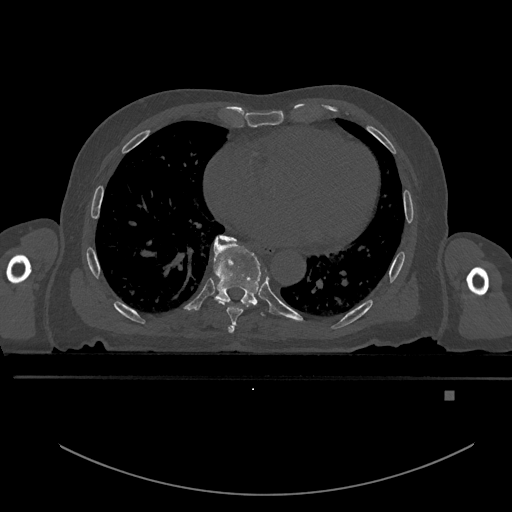
CT including the spine, one axial slice. Slice 226 of 969 in the series (ordered by position). Bone window (W 1800 / L 400 HU). 0.5 mm slice thickness. 512 × 512 image matrix, field of view 456 × 456 mm. Male patient, age 82 years. From the clinical record (not read from this slice): primary cancer: prostate; vertebrae with lytic lesions (as recorded): T11, T9, T8, T2.
Annotated regions visible in this slice (semi-automatically segmented with operator editing):
- T6 vertebra: box from (x=228, y=326) to (x=234, y=333) px
- T7 vertebra: (x=218, y=235)–(x=267, y=325)
- T8 vertebra: (x=213, y=236)–(x=261, y=308)